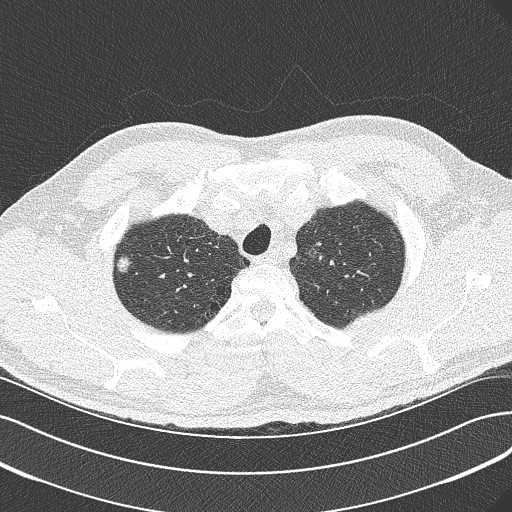
Chest CT (low-dose screening protocol), one axial image. Baseline screening round. Lung window (W 1500 / L -600 HU). 1 mm slice thickness. Lung (sharp) reconstruction kernel (B50f). 120 kVp. Slice 45 of 342 in the series. Male, age 56 years at enrolment. Current smoker at enrolment.
• Expert reader's lesion annotation, bounding box [x1, y1, x2, y2] px = [105, 248, 144, 285].
• The exam's reader record, not a measurement of the box and not confirmed to be the same lesion: non-calcified nodule or mass ≥4 mm, right upper lobe, 10 × 7 mm, spiculated (stellate) margins, soft tissue attenuation.
• Lung cancer was diagnosed 517 days after this screen (after the second annual screen): bronchiolo-alveolar carcinoma, non-mucinous, right upper lobe, moderately differentiated (G2), stage IIIB (AJCC 6th edition), 10 mm at pathology.